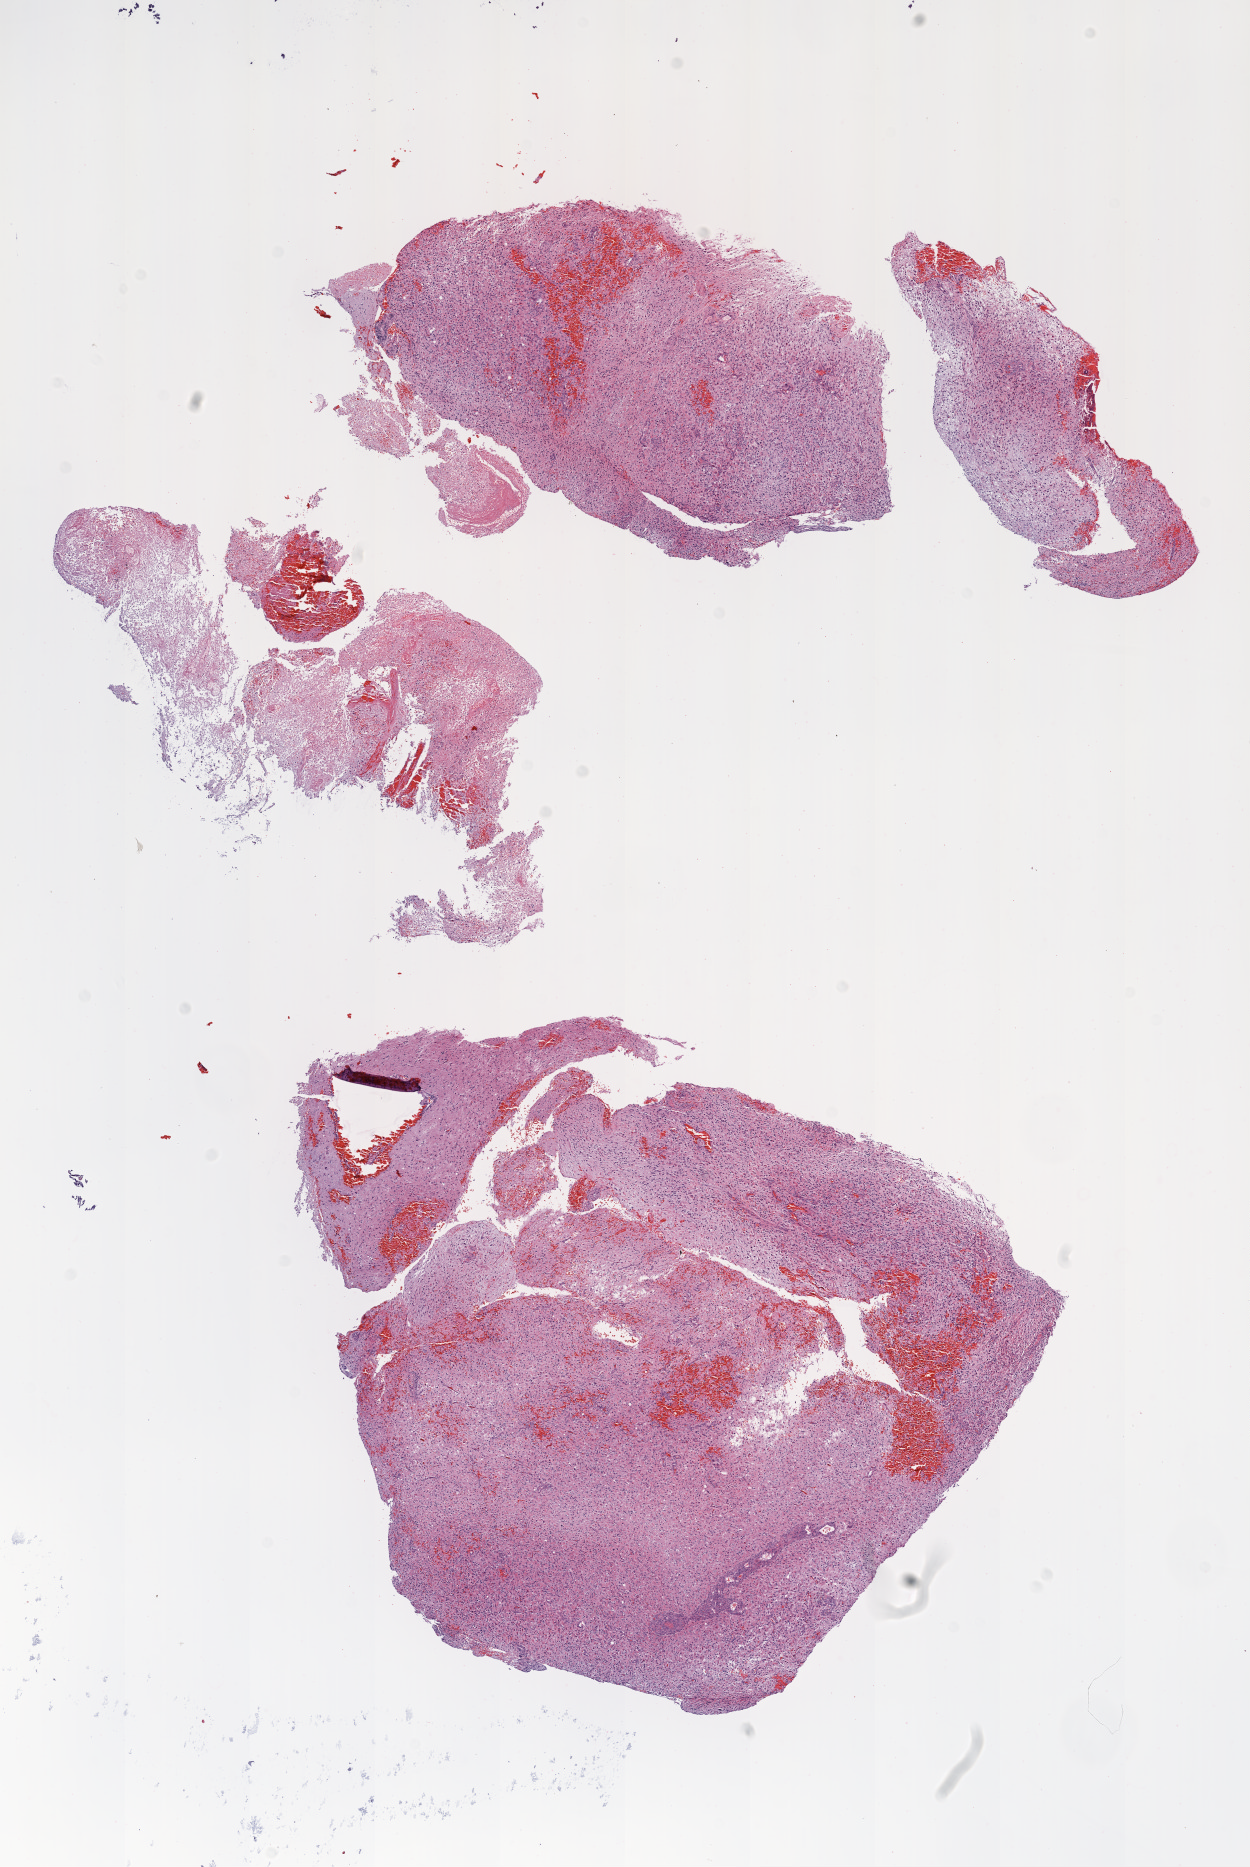
H&E-stained whole-slide image, low-resolution overview of the scanned area, about 10.0 x 15.0 mm (acquisition: 20x scan). Formalin-fixed paraffin-embedded (FFPE) diagnostic section. Sample: primary tumour, brain. Patient: male, age at initial diagnosis 43 years.
Pathologic diagnosis: Glioblastoma.